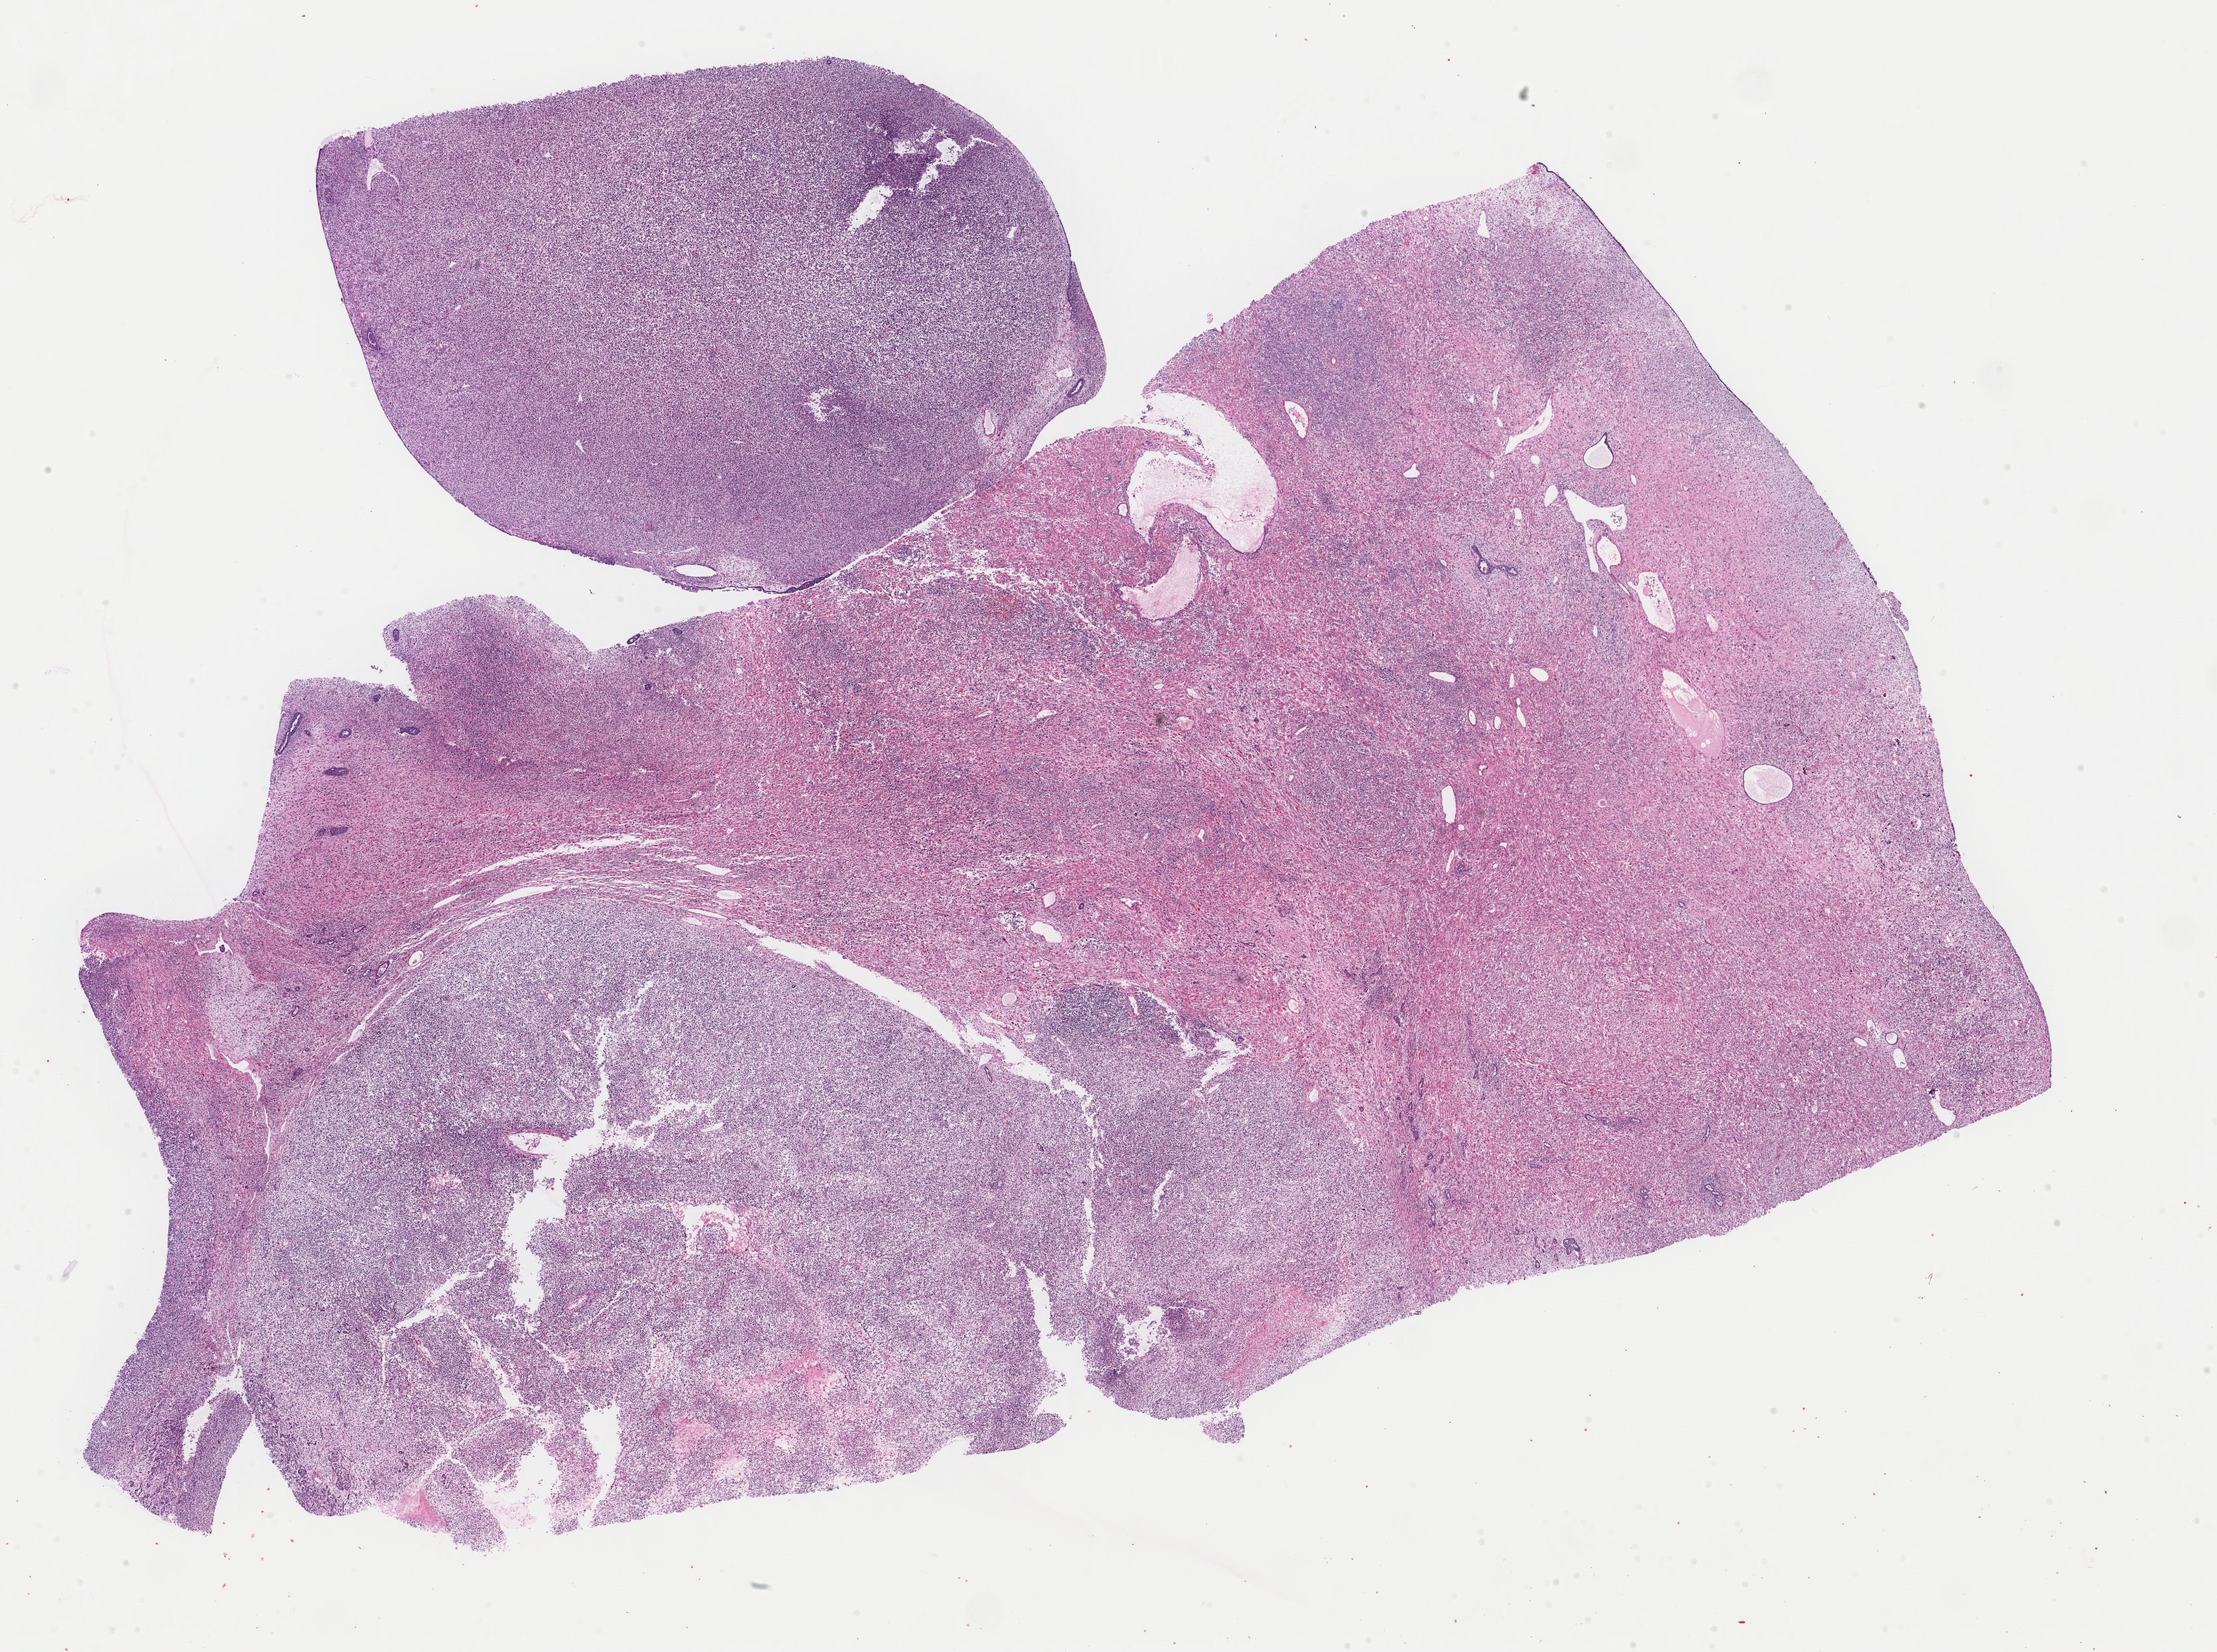
Digitized Hematoxylin and eosin (H&E) stained tissue section (whole slide), whole scanned area (about 26.3 x 19.6 mm, acquisition: 40x scan) shown as a low-resolution overview. Formalin-fixed paraffin-embedded (FFPE) diagnostic section. Sample: primary tumour, uterus. Patient: female, age at initial diagnosis 61 years.
Diagnosis: Mullerian mixed tumor.